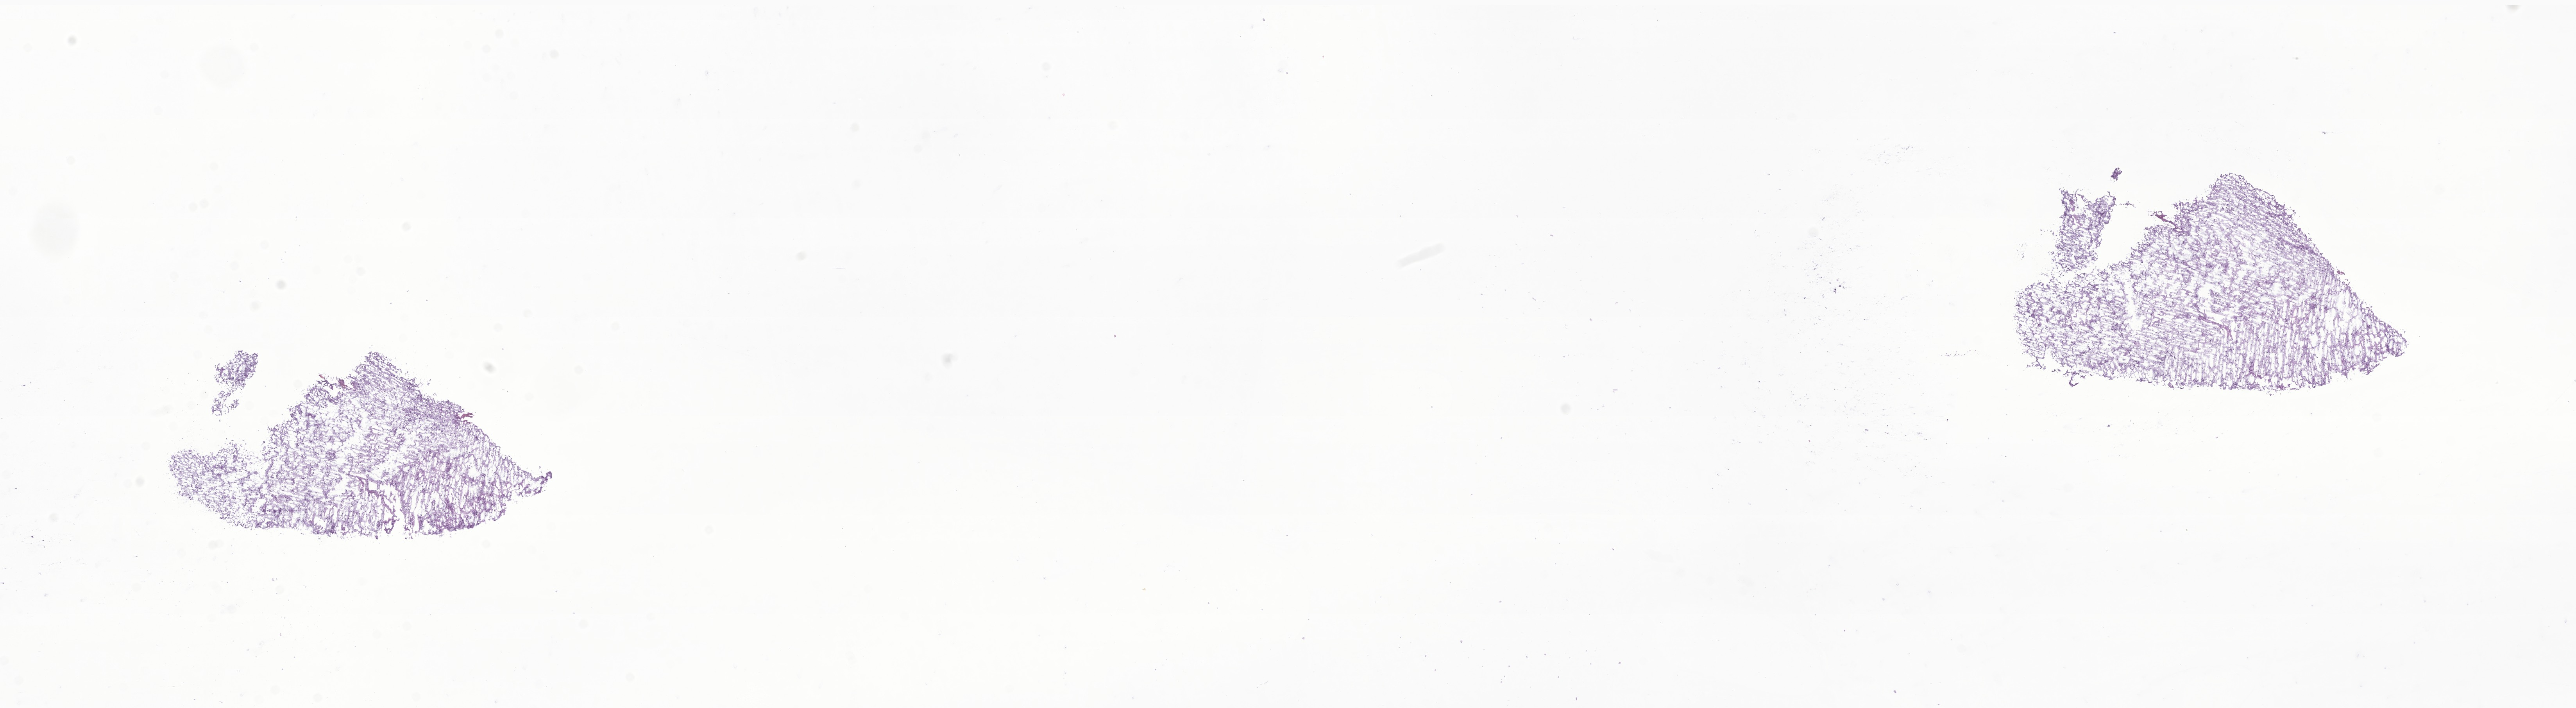
Digitized H&E-stained section of tumor tissue from the brain — whole scanned area (about 27.8 x 7.6 mm) shown as a low-resolution overview. Frozen section. Patient male; age 112 months (9 years 4 months).
- recorded diagnosis: Pilocytic astrocytoma